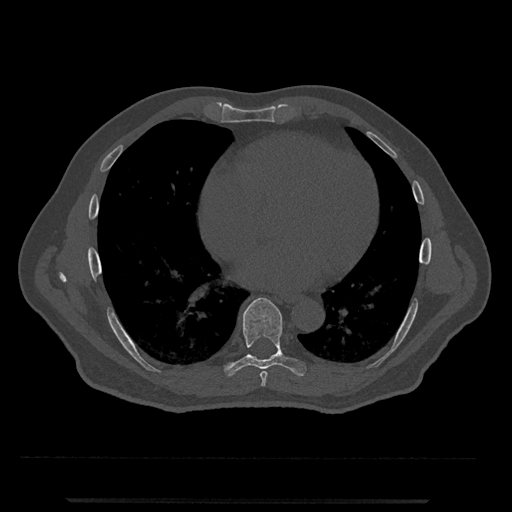
CT including the spine, one axial slice. Slice 632 of 797 in the series (ordered by position). Reconstruction kernel Br40s/3. 120 kVp. Bone window (W 1800 / L 400 HU). 0.5 mm slice thickness. 512 × 512 image matrix, field of view 419 × 419 mm. Patient: male, 63 years. From the clinical record (not read from this slice): primary cancer: prostate.
Outlined on this slice (semi-automatically segmented with operator editing):
- T7 vertebra: bounding box [x1, y1, x2, y2] px = [260, 371, 268, 387]
- T8 vertebra: [224, 298, 306, 377]